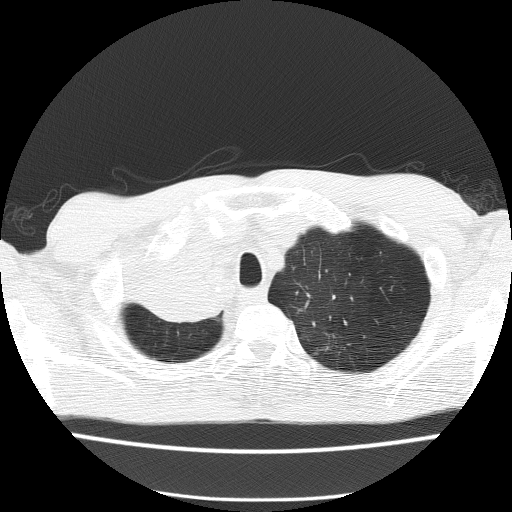
Low-dose screening chest CT, one axial slice. Position 127 of 150 along the scan axis. Reconstruction kernel FC51. 120 kVp. Lung window (W 1500 / L -600 HU). 512 × 512 image matrix, field of view 336 × 336 mm.
Structures marked on this image (expert manual segmentation):
- lesion 1 (tumor, hilum of right lung): box from (x=137, y=255) to (x=225, y=323) px